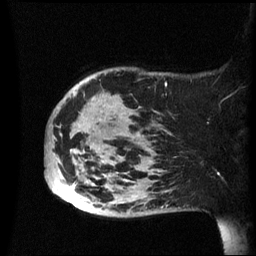
Breast MRI (dynamic contrast-enhanced), one sagittal slice; slice 14 of 60 in the series (ordered by position); dynamic contrast-enhanced series, image 2 of 3 at this slice position (ordered by acquisition); 1.5 T; TE 4.2 ms, TR 8.4 ms; 2.4 mm slice thickness; 256 × 256 image matrix, field of view 230 × 230 mm. Patient: female, 49 years.
Outlined on this slice (semi-automatically segmented with operator editing):
- analysis volume of interest (the breast-tissue region the enhancement analysis was run in; not a lesion): bounding box [x1, y1, x2, y2] px = [45, 67, 174, 217]
- tumour enhancement mask (voxels above the 70 % enhancement threshold inside the analysis volume of interest): [74, 93, 128, 215]